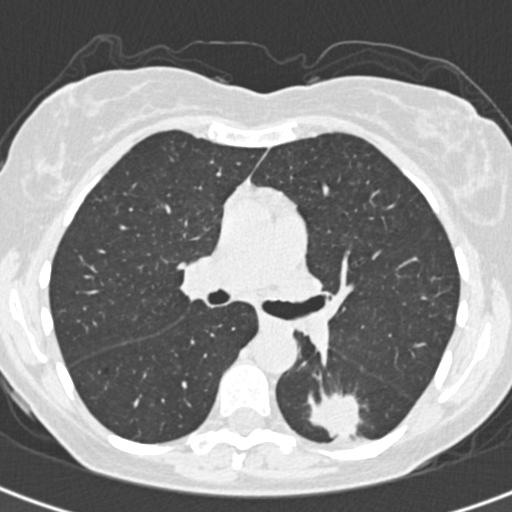
Low-dose screening chest CT, one axial slice; position 202 of 328 along the scan axis; reconstruction kernel B30f; 120 kVp; lung window (W 1500 / L -600 HU); 512 × 512 image matrix, field of view 284 × 284 mm.
Structures marked on this image (outlined manually by an expert reader):
- lesion 1 (tumor, lower lobe of left lung): bounding box (x1, y1, x2, y2) in pixels: (309, 393, 362, 439)